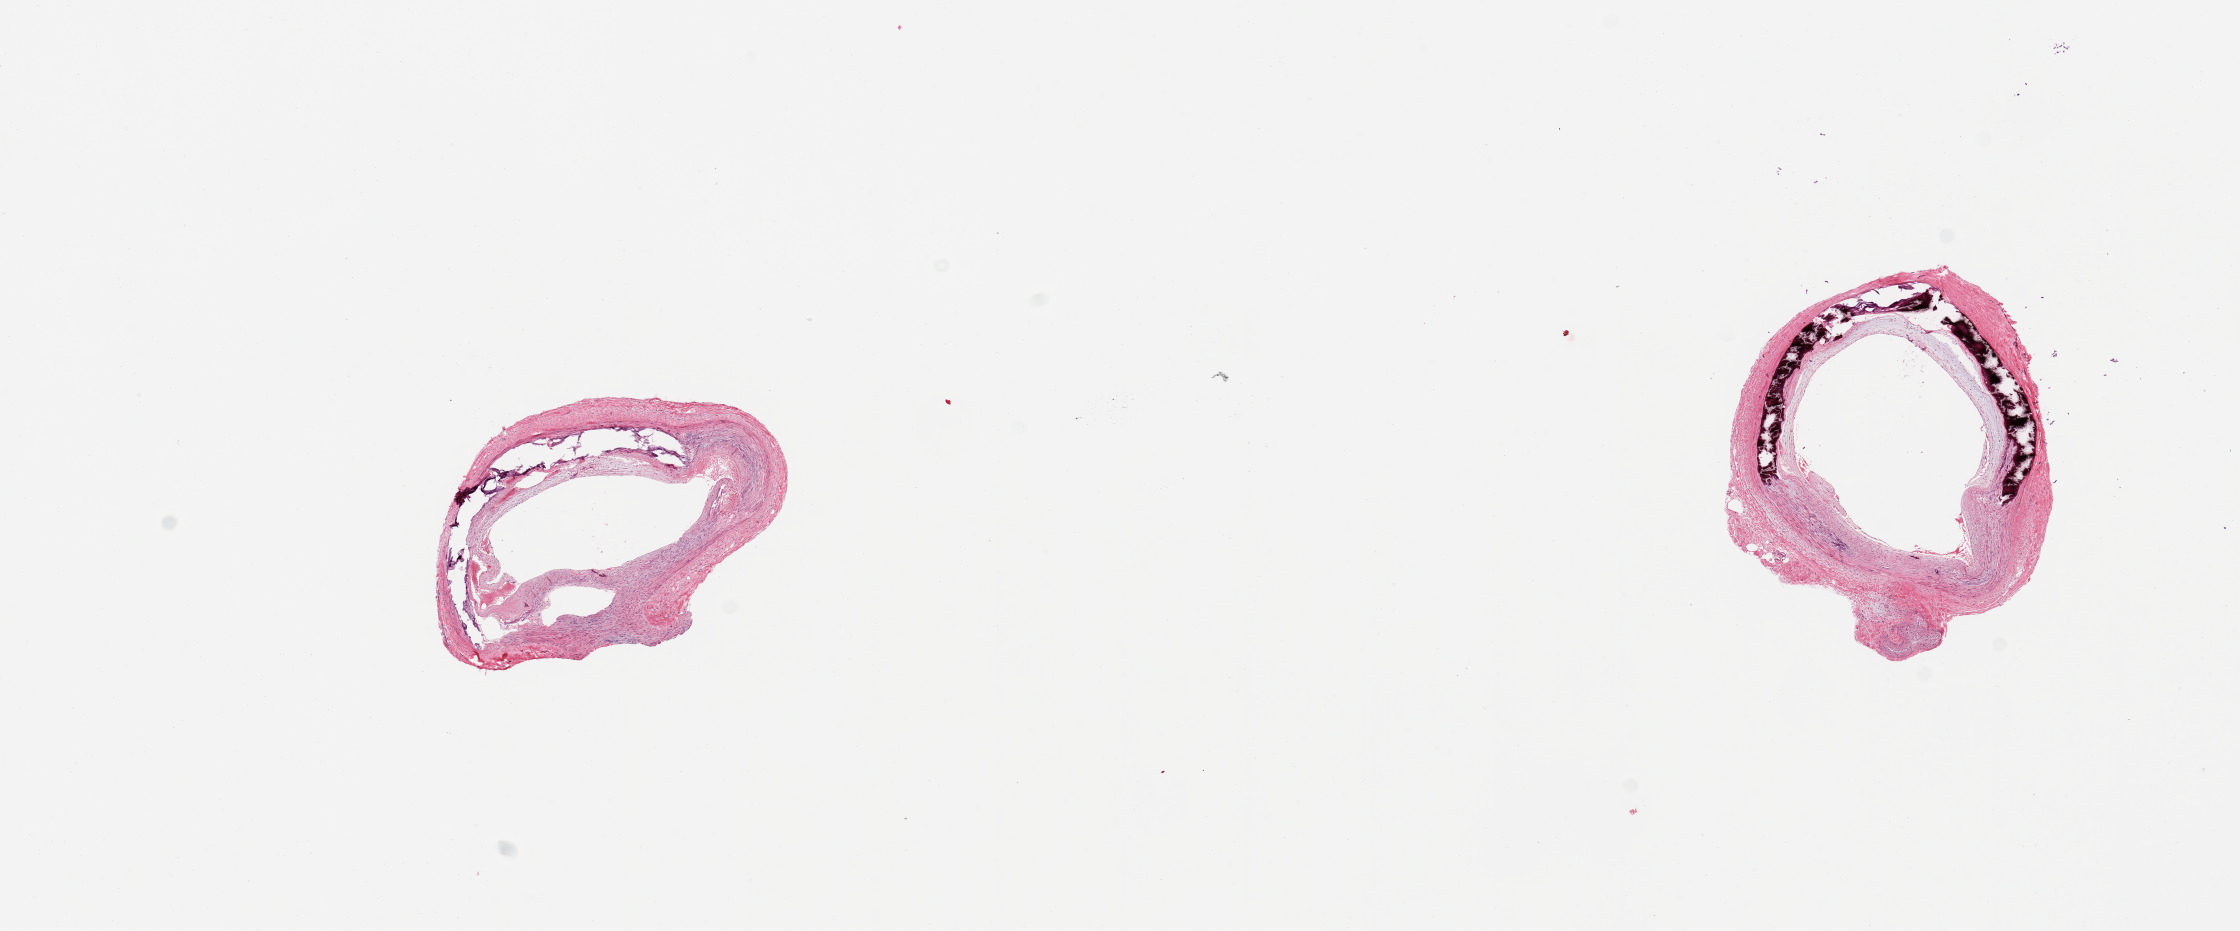
Hematoxylin and eosin (H&E) whole-slide image, shown as a low-resolution overview of the whole scanned area (about 17.7 x 7.4 mm), PAXgene-fixed, paraffin-embedded tissue, target tissue: tibial artery, donor tissue sample. Female donor.
Reviewer comment on this tissue sample: 2 pieces; 40% calcification.